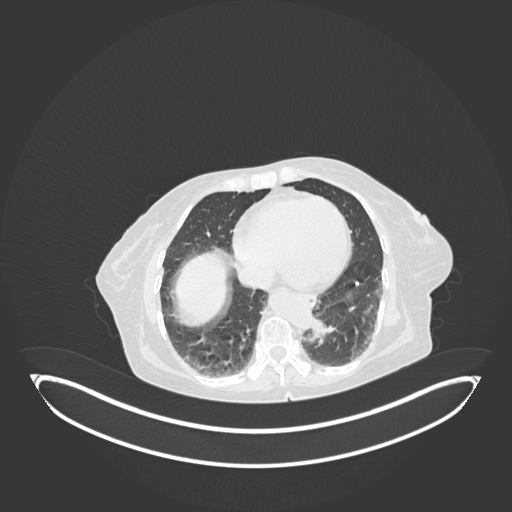
Chest CT, one axial slice; reconstruction kernel B30f; 120 kVp; lung window (W 1500 / L -600 HU); 1 mm slice thickness; 512 × 512 image matrix, field of view 500 × 500 mm. Patient: female, 82 years. Case-level facts recorded for this patient, not image findings: clinical TNM (as recorded): T1b N0 M1.
Structures marked on this image (bounding box drawn by a radiologist):
- lung tumour (recorded histology: adenocarcinoma): bounding box <308,315,334,342> (left, top, right, bottom; pixels)